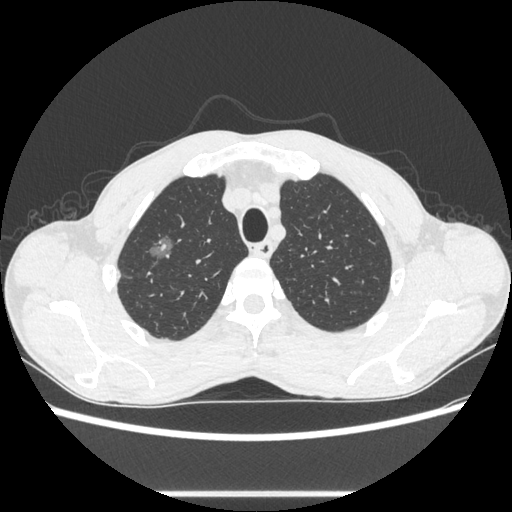
Chest CT, one axial slice. Position 492 of 600 along the scan axis. 100 kVp. Lung window (W 1500 / L -600 HU). 0.62 mm slice thickness. 512 × 512 image matrix, field of view 357 × 357 mm. Male patient, age 54 years. From the clinical record (not read from this slice): clinical TNM (as recorded): T1a N0 M0.
Annotated regions visible in this slice (rectangle marked by the reading radiologist):
- lung tumour (recorded histology: adenocarcinoma): box from (x=144, y=230) to (x=178, y=265) px